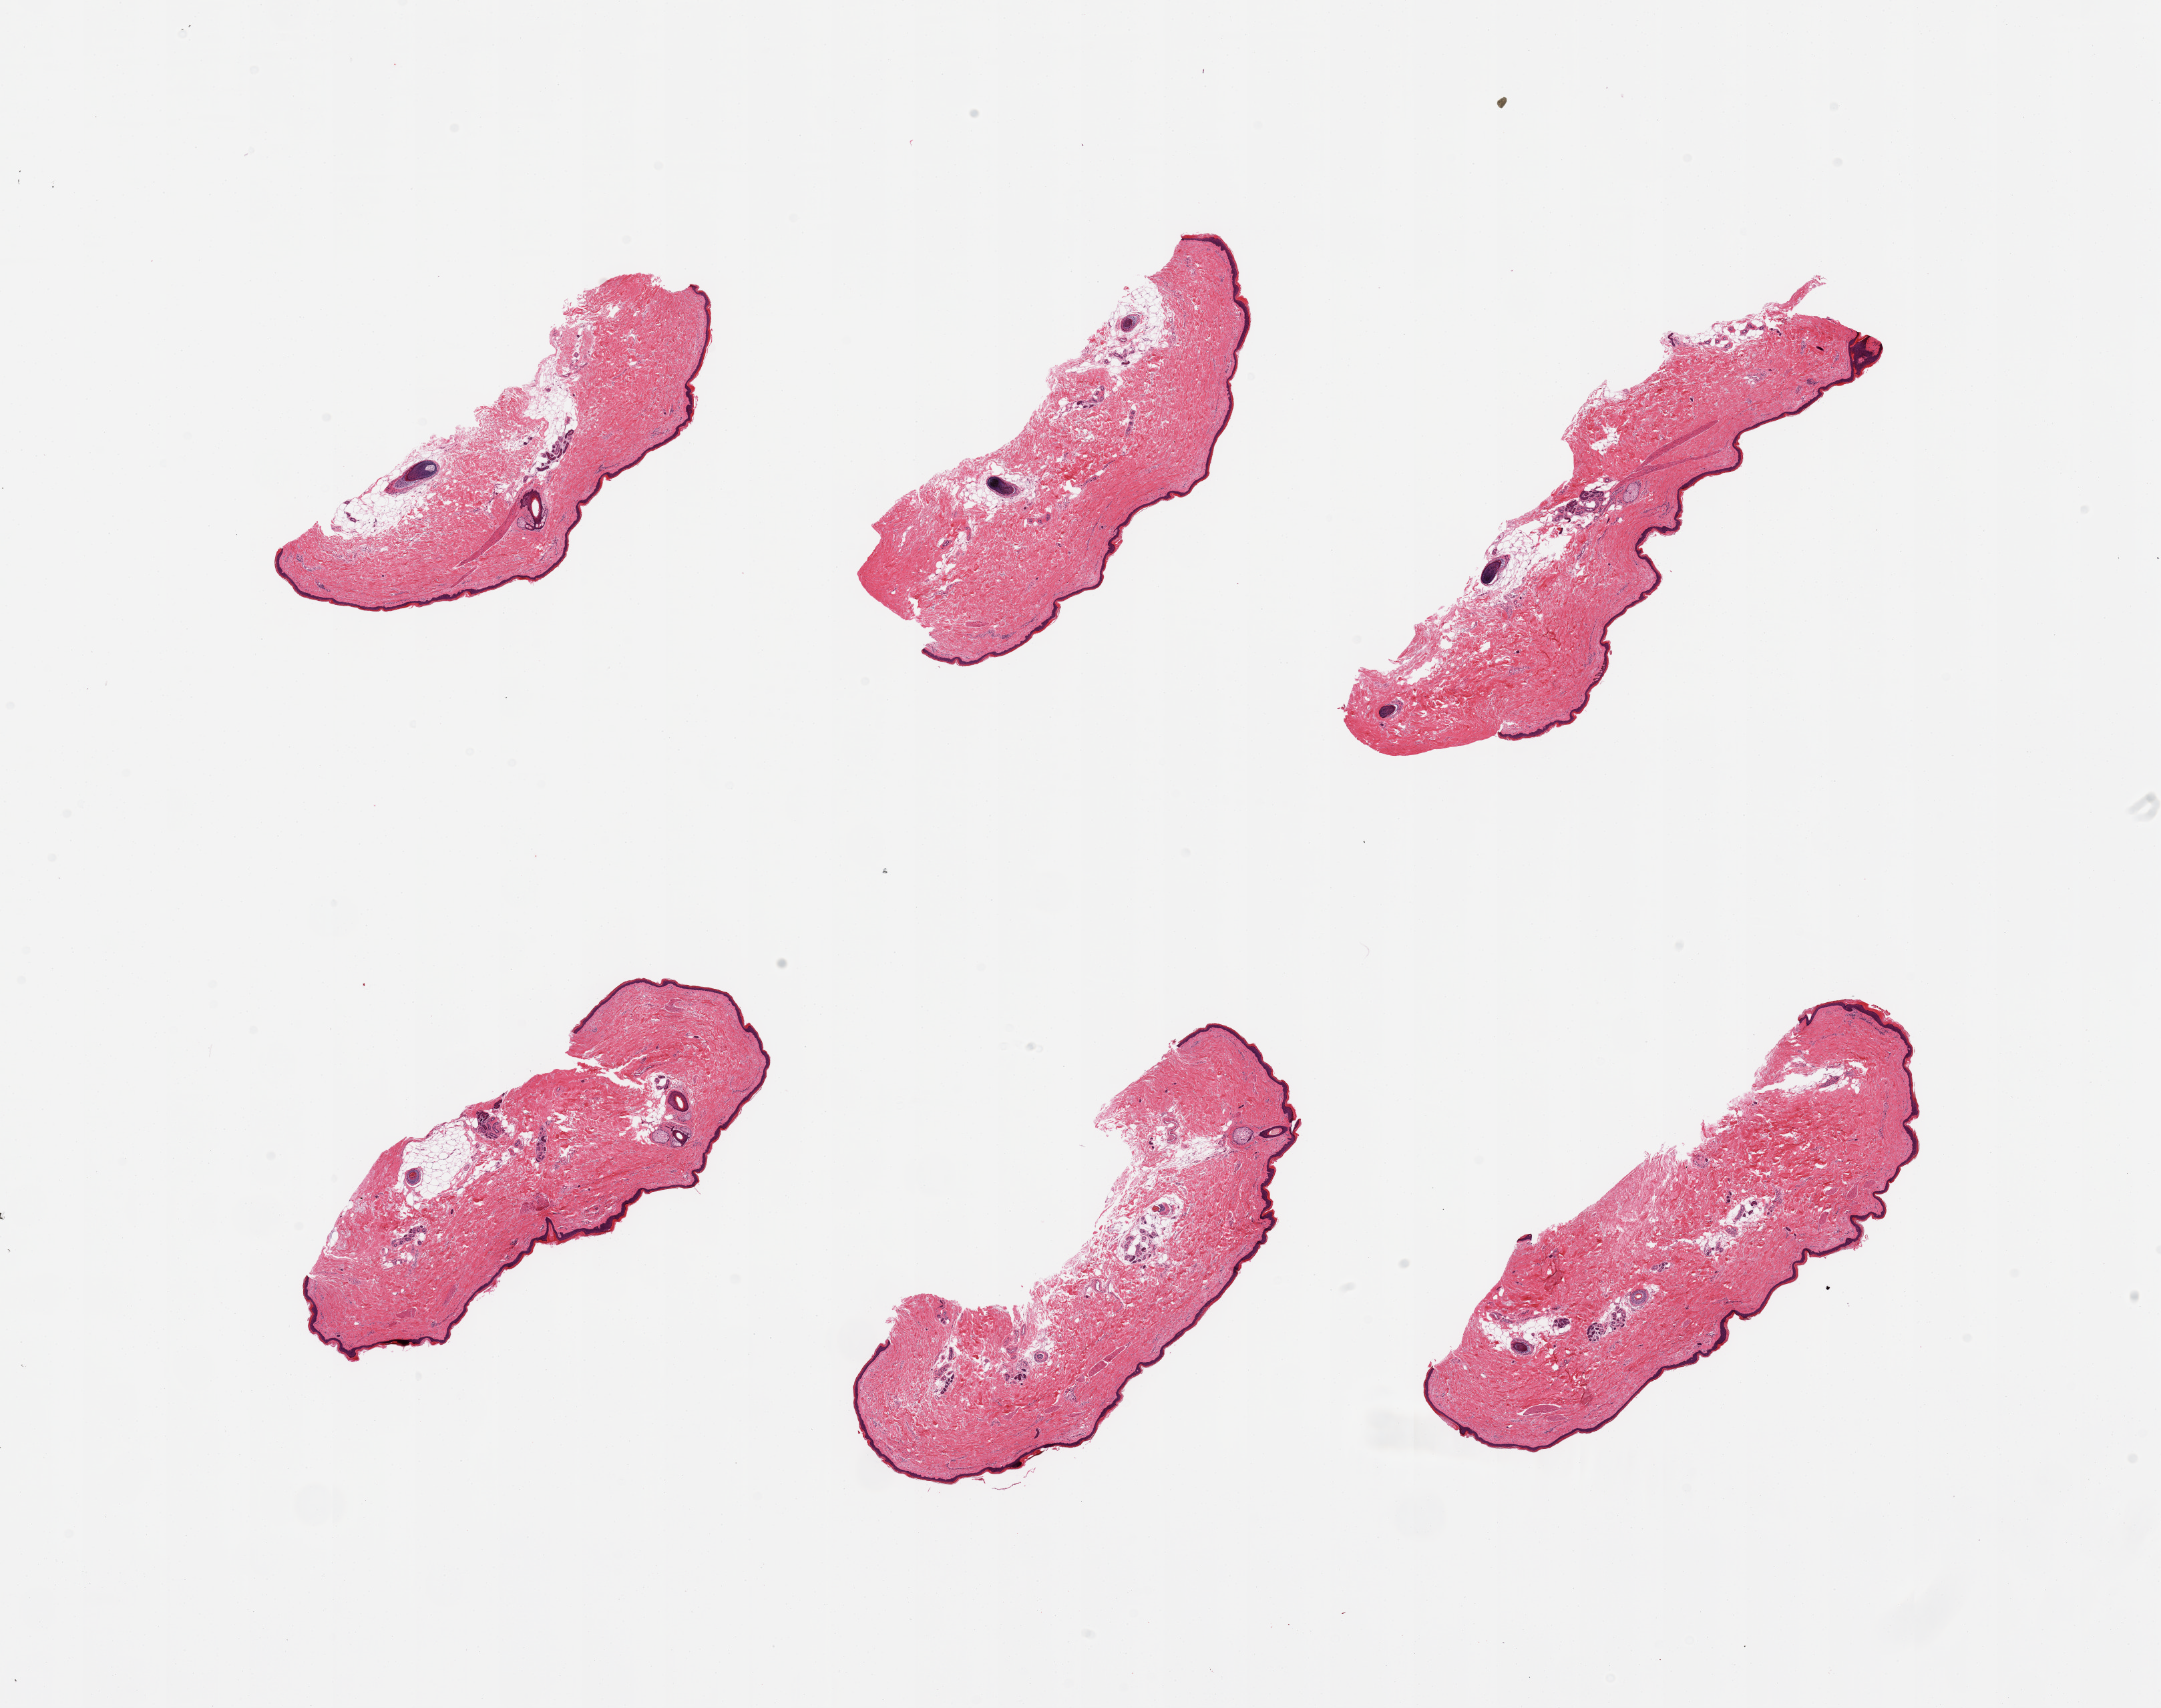
Digitized H&E-stained section — a low-resolution overview of the entire scanned area, about 25.6 x 20.2 mm (acquisition: 20x scan). PAXgene-fixed paraffin-embedded (PFPE) section. Target tissue: skin of lower leg. Tissue donor sample. Donor sex: male.
* review note (as recorded): 6 pieces, minimal fat, squamous epitheliums is ~40 microns